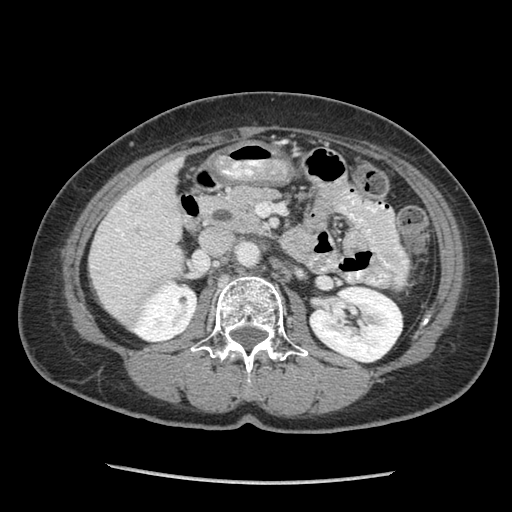
Contrast-enhanced abdominal CT (liver protocol), one axial slice. Slice 29 of 105 in the series (ordered by position). Reconstruction kernel STANDARD. 140 kVp. Soft-tissue window (W 400 / L 40 HU). 2.5 mm slice thickness. 512 × 512 image matrix, field of view 340 × 340 mm. Case-level facts recorded for this patient, not image findings: diagnosis: hepatocellular carcinoma (patient treated with transarterial chemoembolisation; whether this scan precedes or follows treatment is not stated here); TNM stage (as recorded): Stage-I; Child-Pugh class: A; tumour differentiation: moderately differentiated; tumour nodularity: uninodular.
Annotated regions visible in this slice (semi-automatic segmentation, software-assisted and operator-edited):
- liver parenchyma outside the tumour (the mass and vessels are separate outlines, so this box may not span the whole liver): box from (x=90, y=154) to (x=184, y=316) px
- liver vessels: (x=92, y=192)–(x=177, y=308)